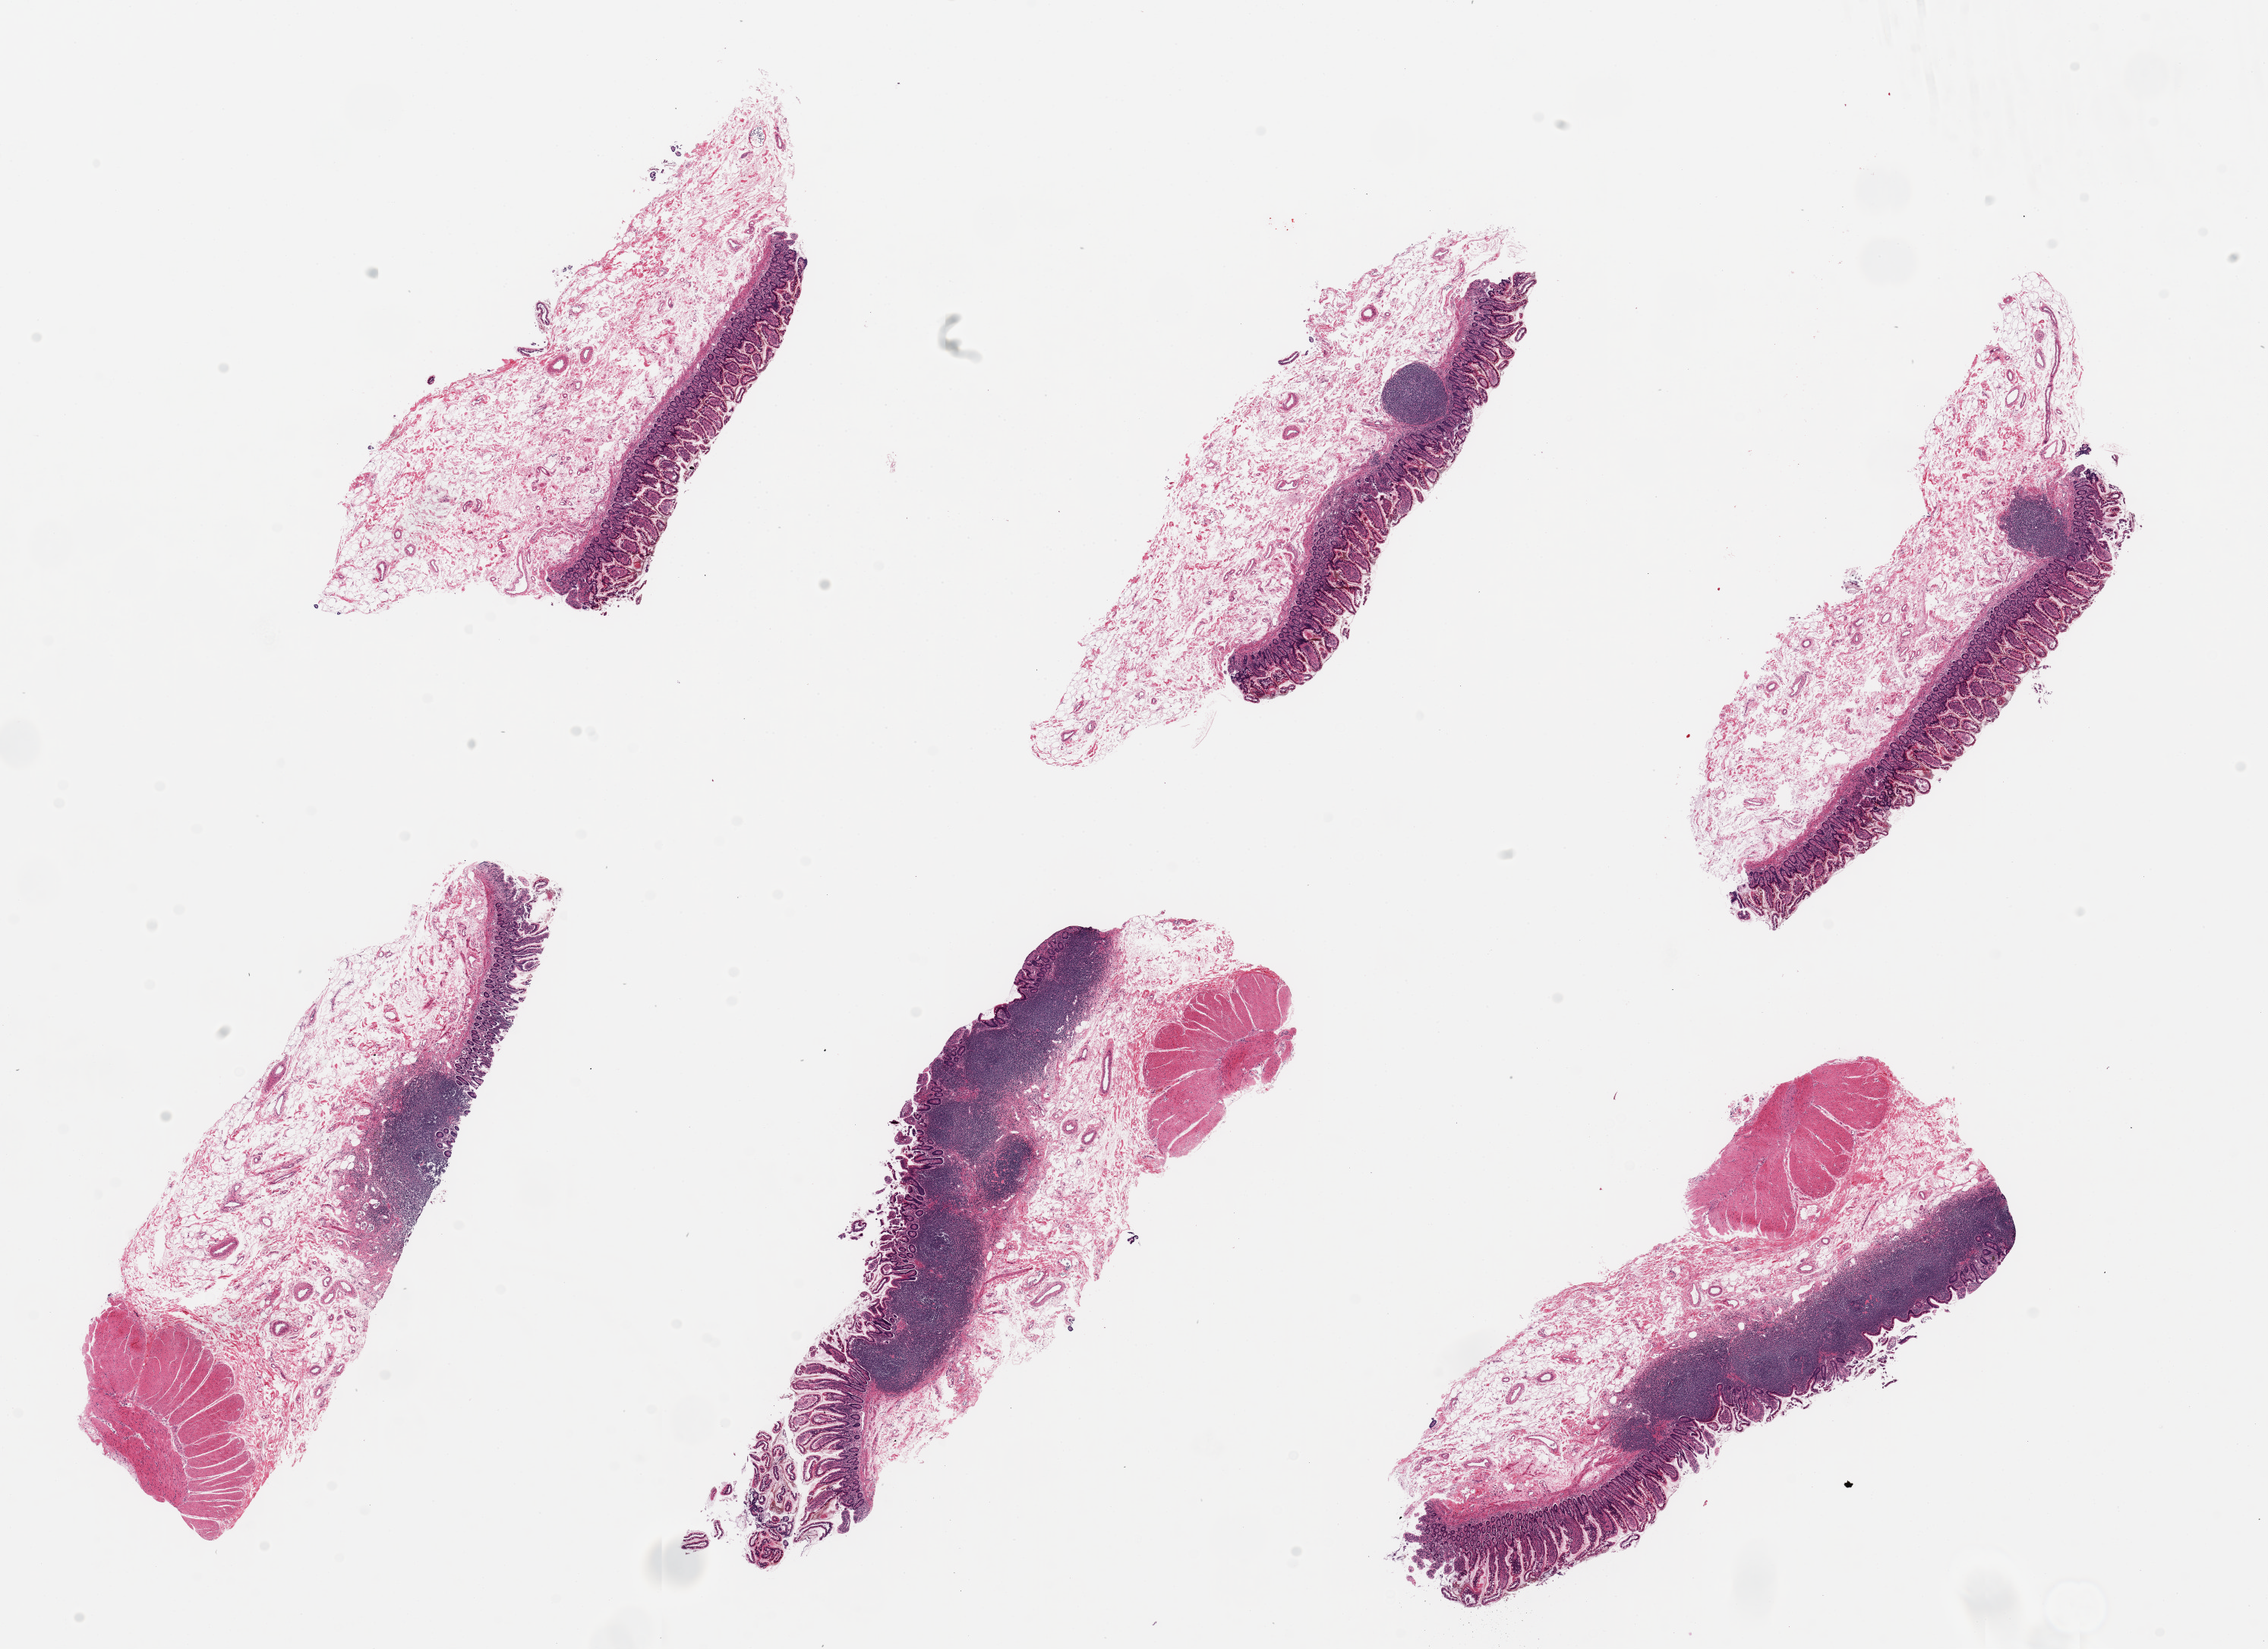
Digitized haematoxylin and eosin-stained section — whole scanned area (about 23.6 x 17.2 mm) shown as a low-resolution overview, PAXgene-fixed, paraffin-embedded tissue, sampled site (target tissue): ileum, donor tissue sample. Donor: male.
• review note (as recorded): 6 pieces, up to 8x3mm; lymphoid tissue with slight autolysis, mucosa has moderate autolysis; abundant lymphoid tissue, up to 5 x 0.8 mm in 2 pieces, small focal lymphoid nodules in 3 and none in 1 piece; ~20% untrimmed muscularis in 3 pieces